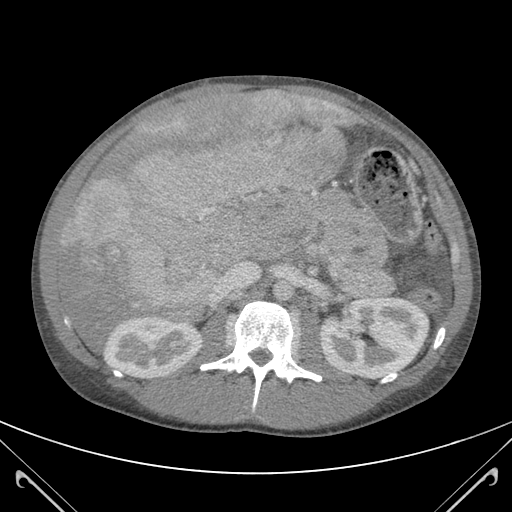
Contrast-enhanced abdominal CT (liver protocol), one axial slice; position 63 of 118 along the scan axis; 120 kVp; soft-tissue window (W 400 / L 40 HU); 3 mm slice thickness; 512 × 512 image matrix, field of view 380 × 380 mm. Case-level facts recorded for this patient, not image findings: diagnosis: hepatocellular carcinoma (patient treated with transarterial chemoembolisation; whether this scan precedes or follows treatment is not stated here); TNM stage (as recorded): Stage-IIIB; Child-Pugh class: A; tumour nodularity: uninodular.
Annotated regions visible in this slice (semi-automatically segmented with operator editing):
- abdominal aorta: bounding box (x1, y1, x2, y2) in pixels: (273, 280, 293, 301)
- liver parenchyma outside the tumour (the mass and vessels are separate outlines, so this box may not span the whole liver): (56, 90, 355, 350)
- mass: (66, 92, 342, 325)
- liver vessels: (63, 101, 344, 306)